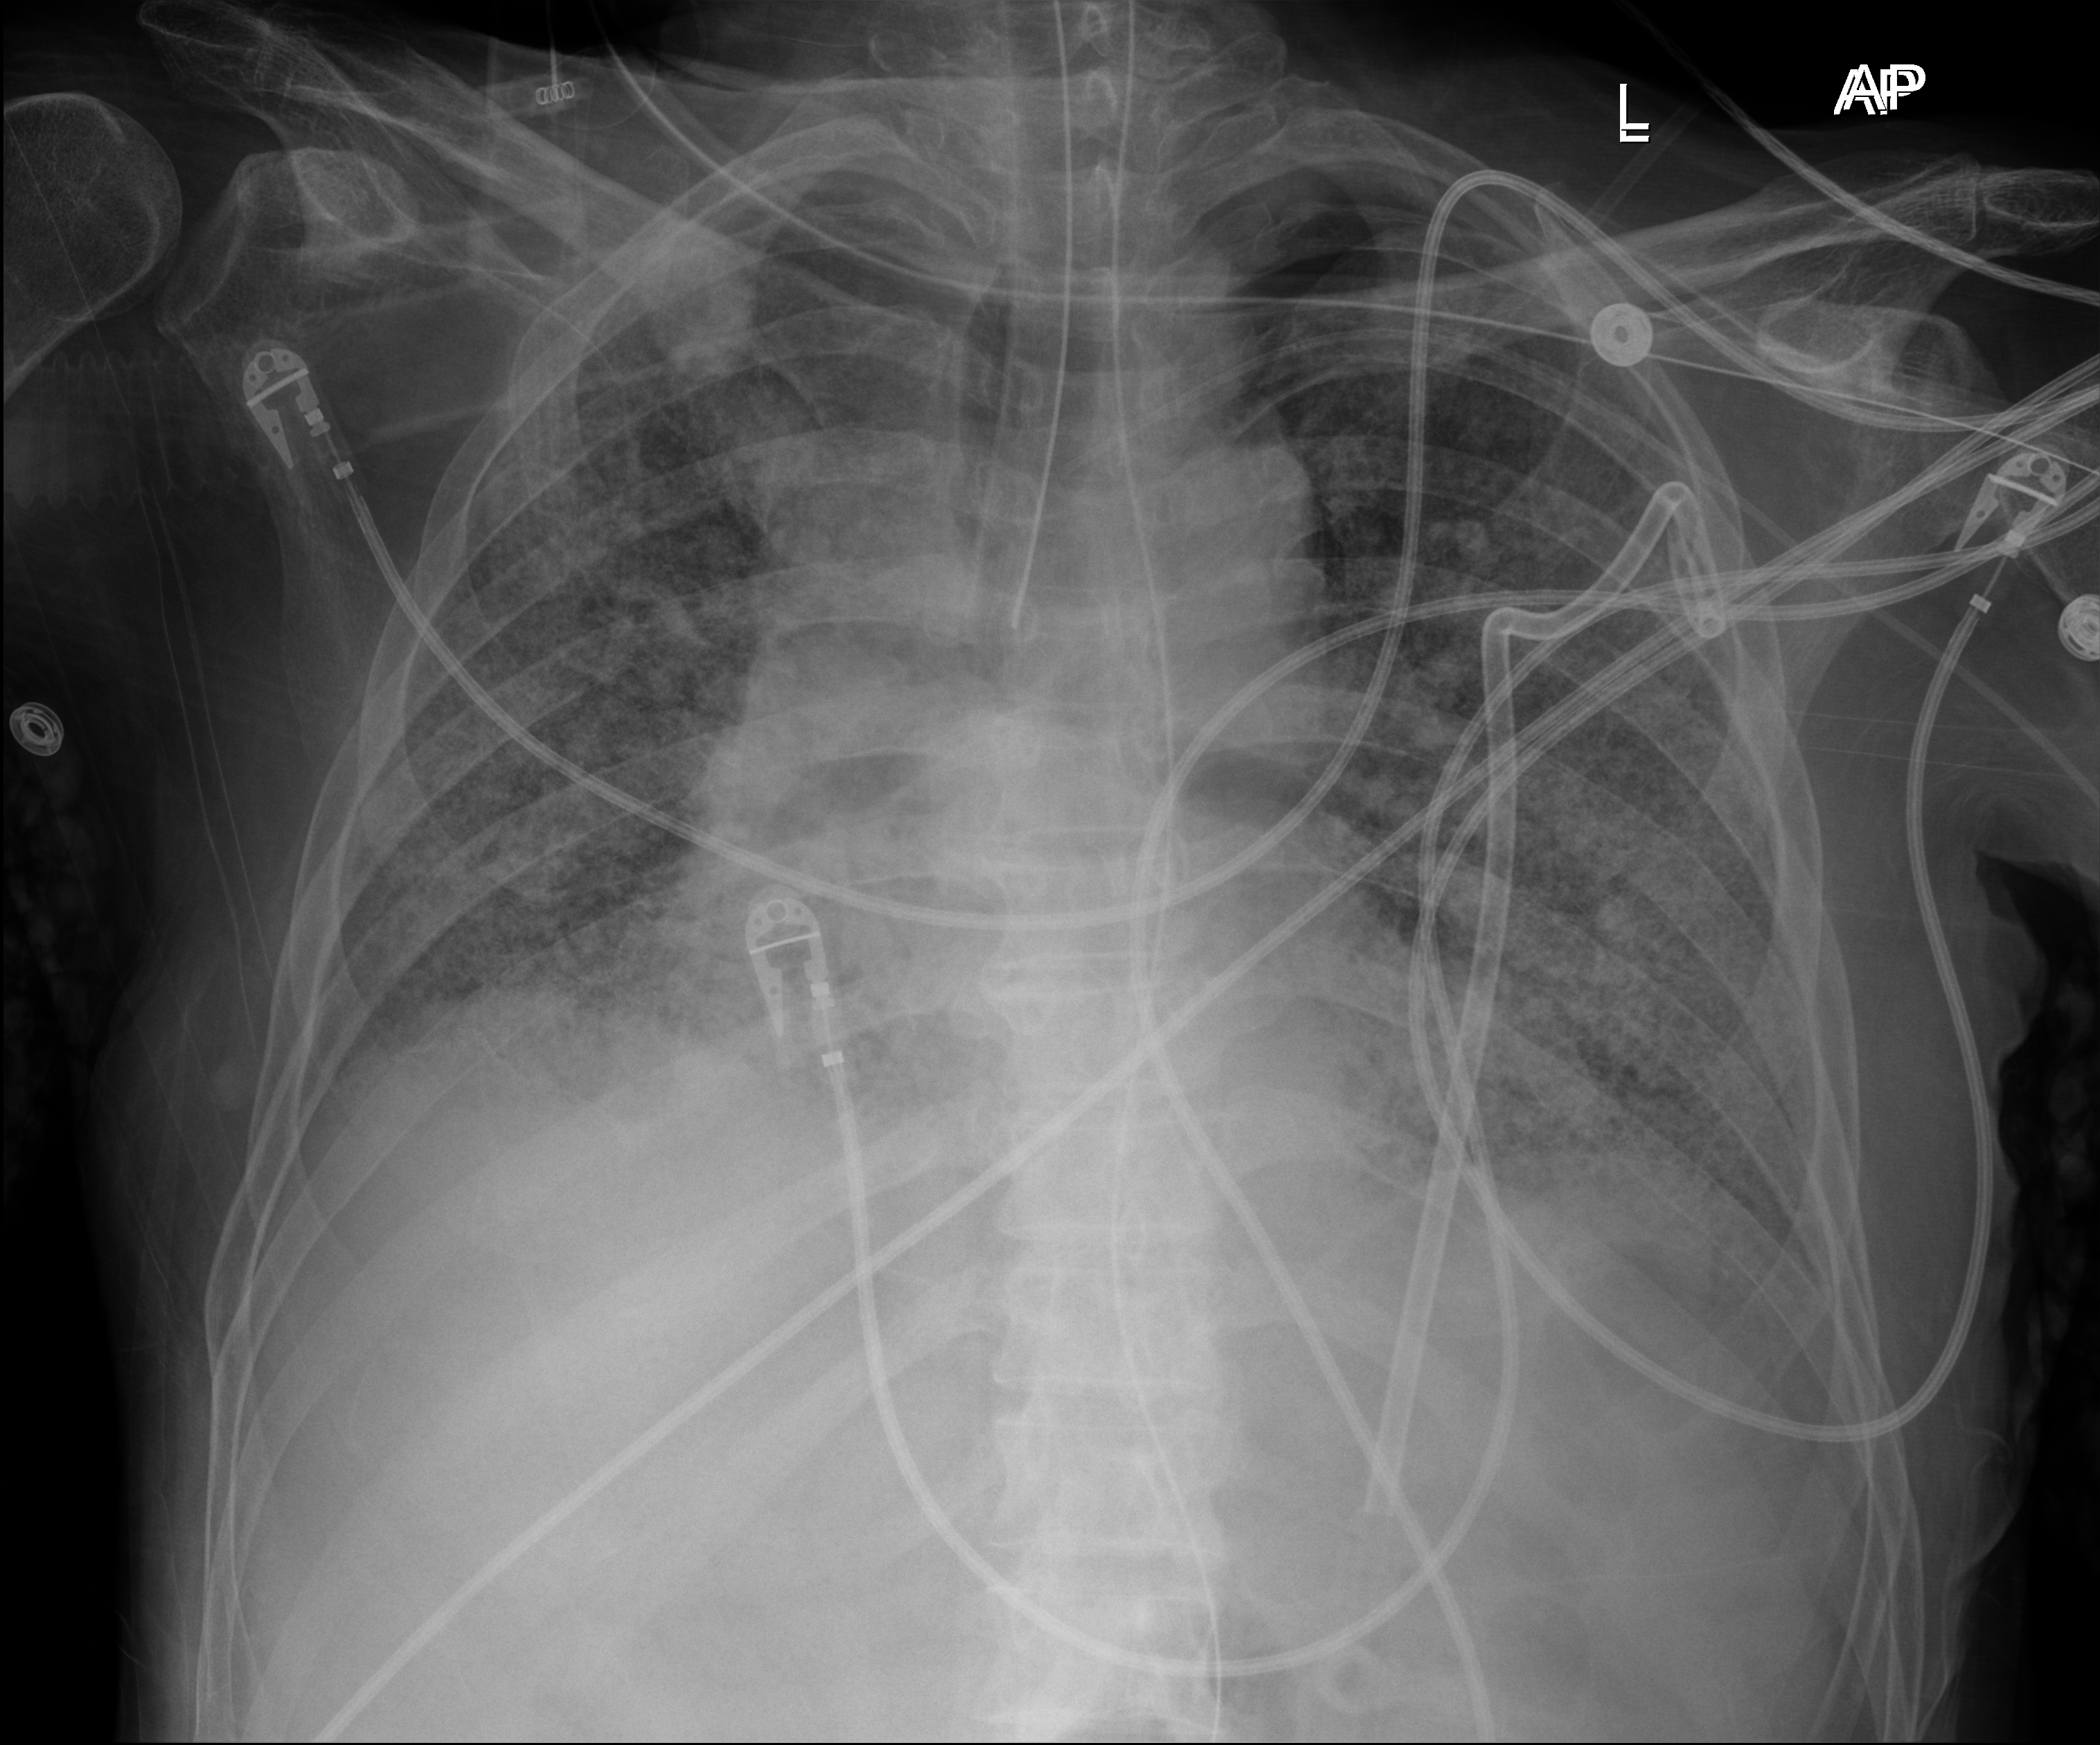
Bedside chest radiograph (digital radiography); anteroposterior (AP) projection. Male patient hospitalised with COVID-19, age 60–74 years.
From the hospital-stay record, not from the radiograph (when in the stay this image was taken is not recorded): mechanically ventilated during this hospital stay: yes; admitted to intensive care during this hospital stay: yes.